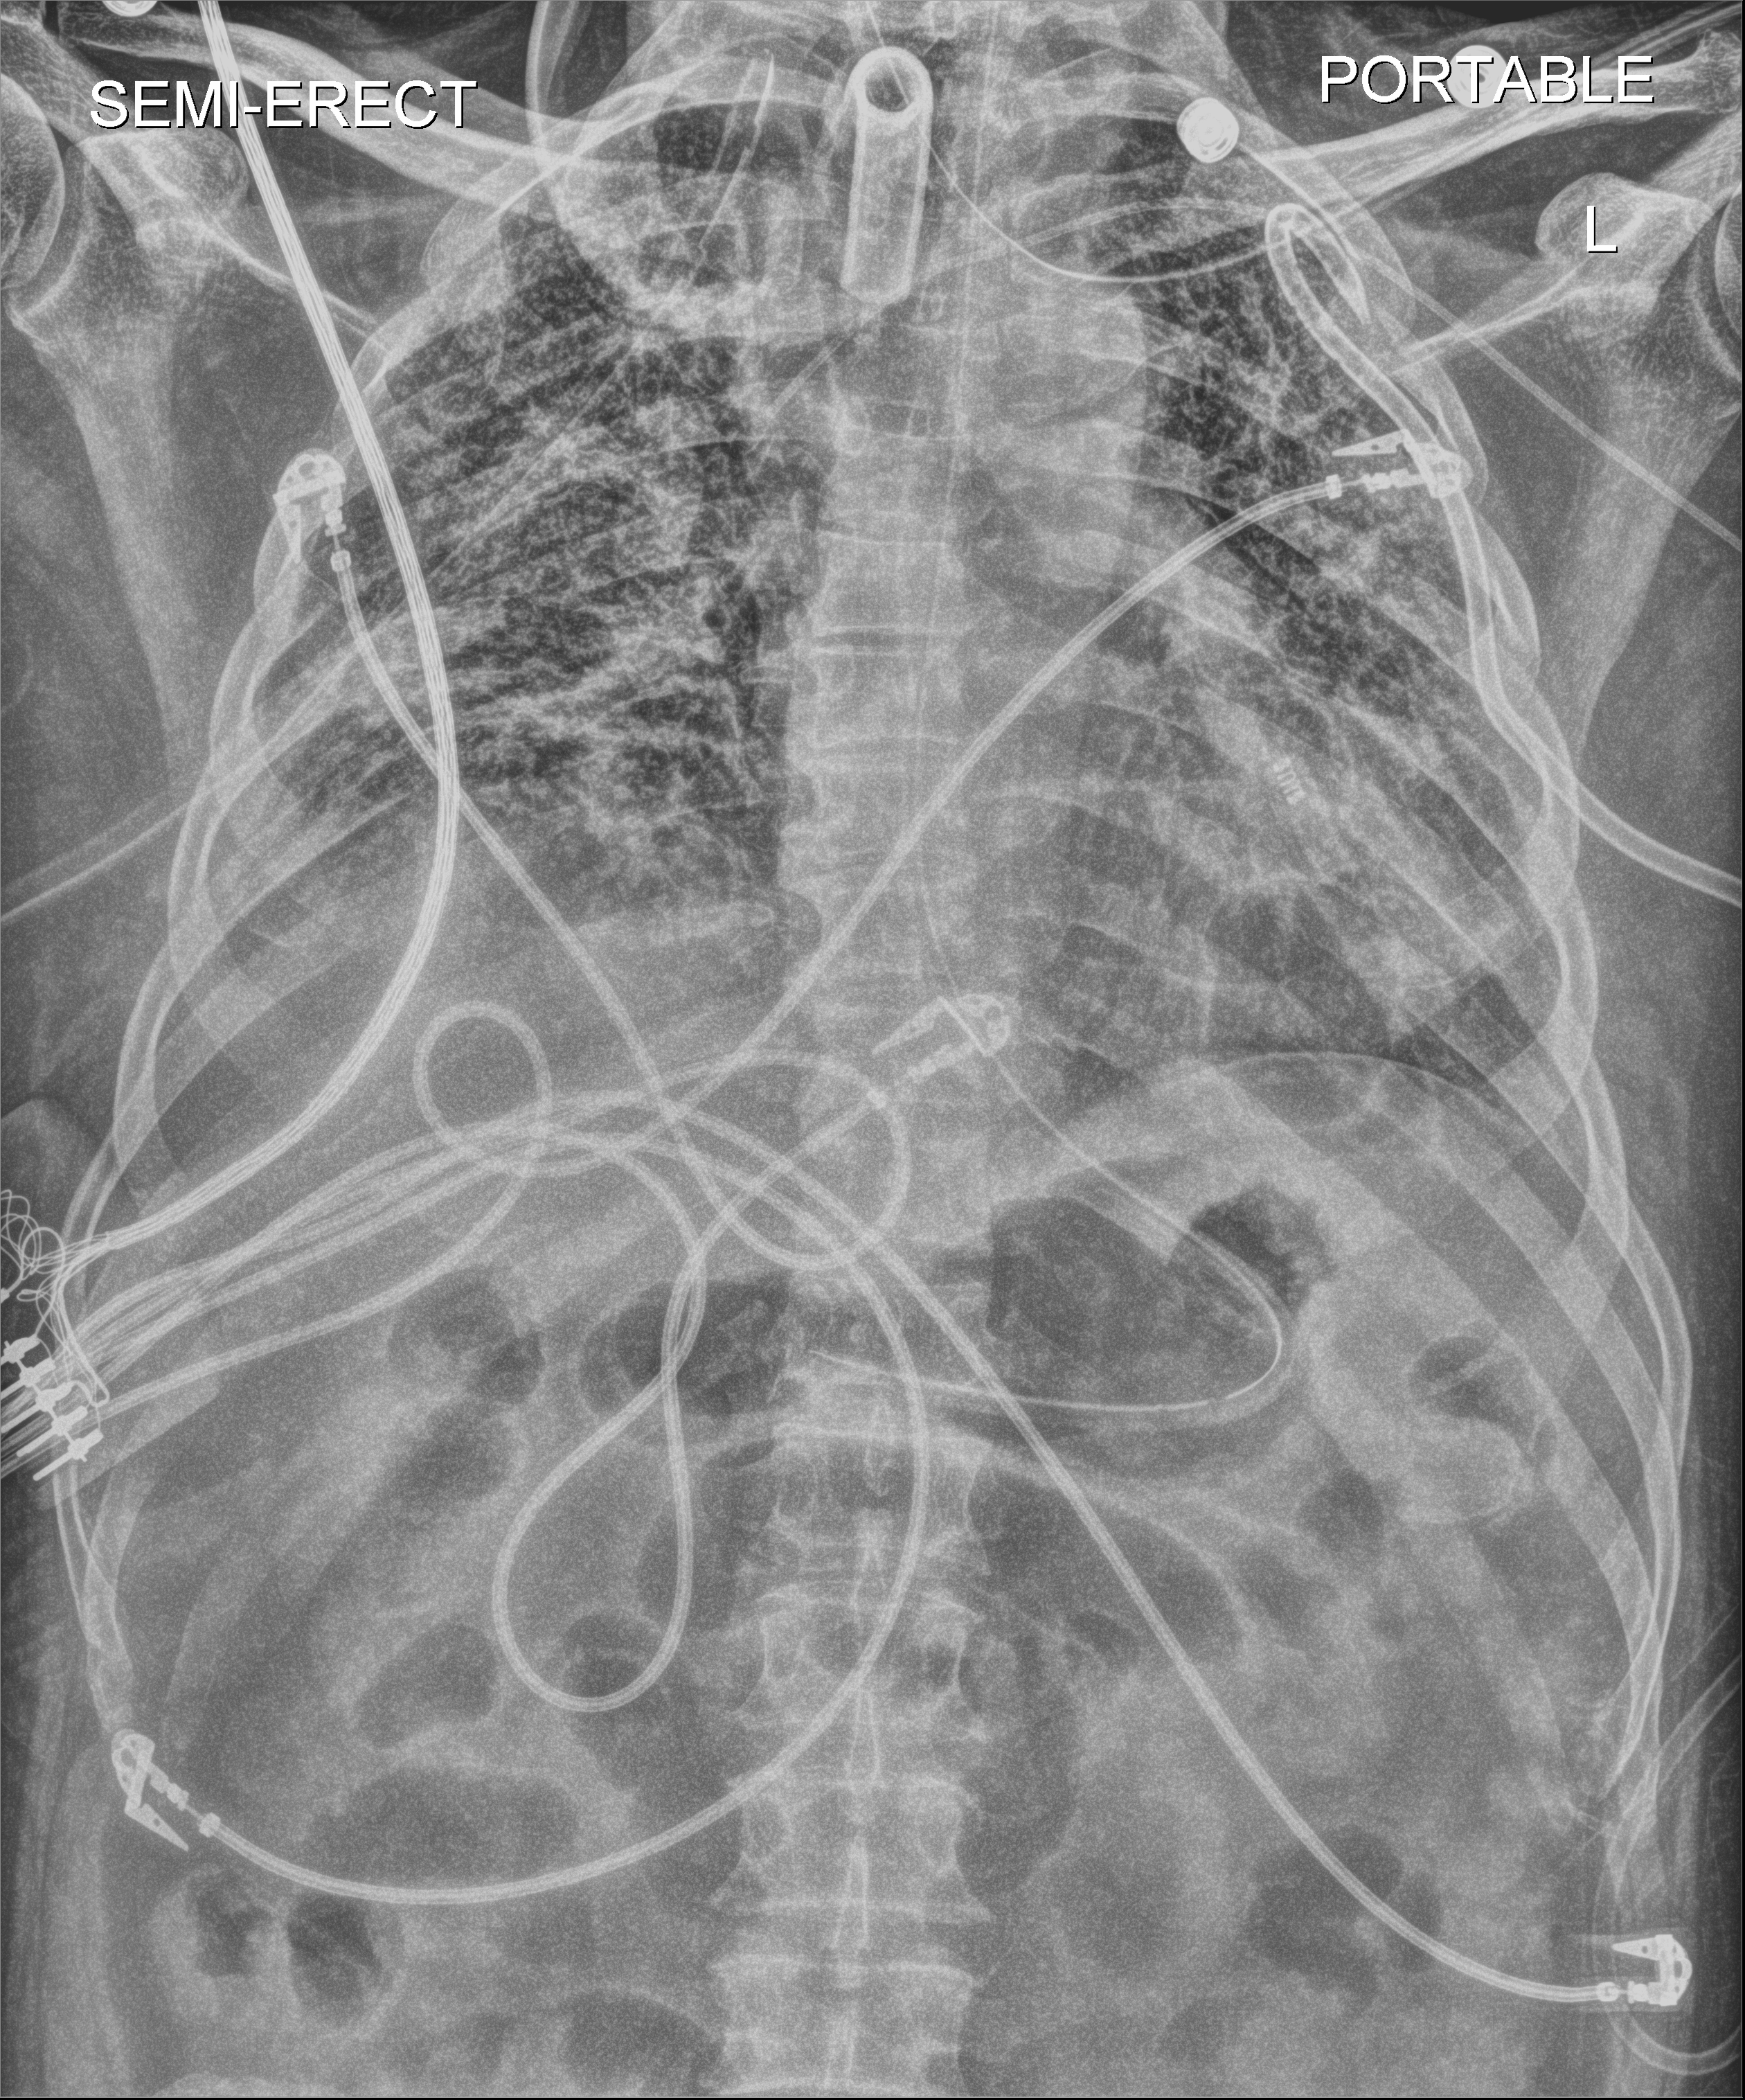
Portable chest radiograph. Male patient hospitalised with COVID-19, age 18–59 years.
Admission-level facts for this patient (not findings on this image; timing relative to this image not recorded):
- mechanically ventilated during this hospital stay: yes
- chronic kidney disease (admission record): no
- other chronic lung disease (admission record): no